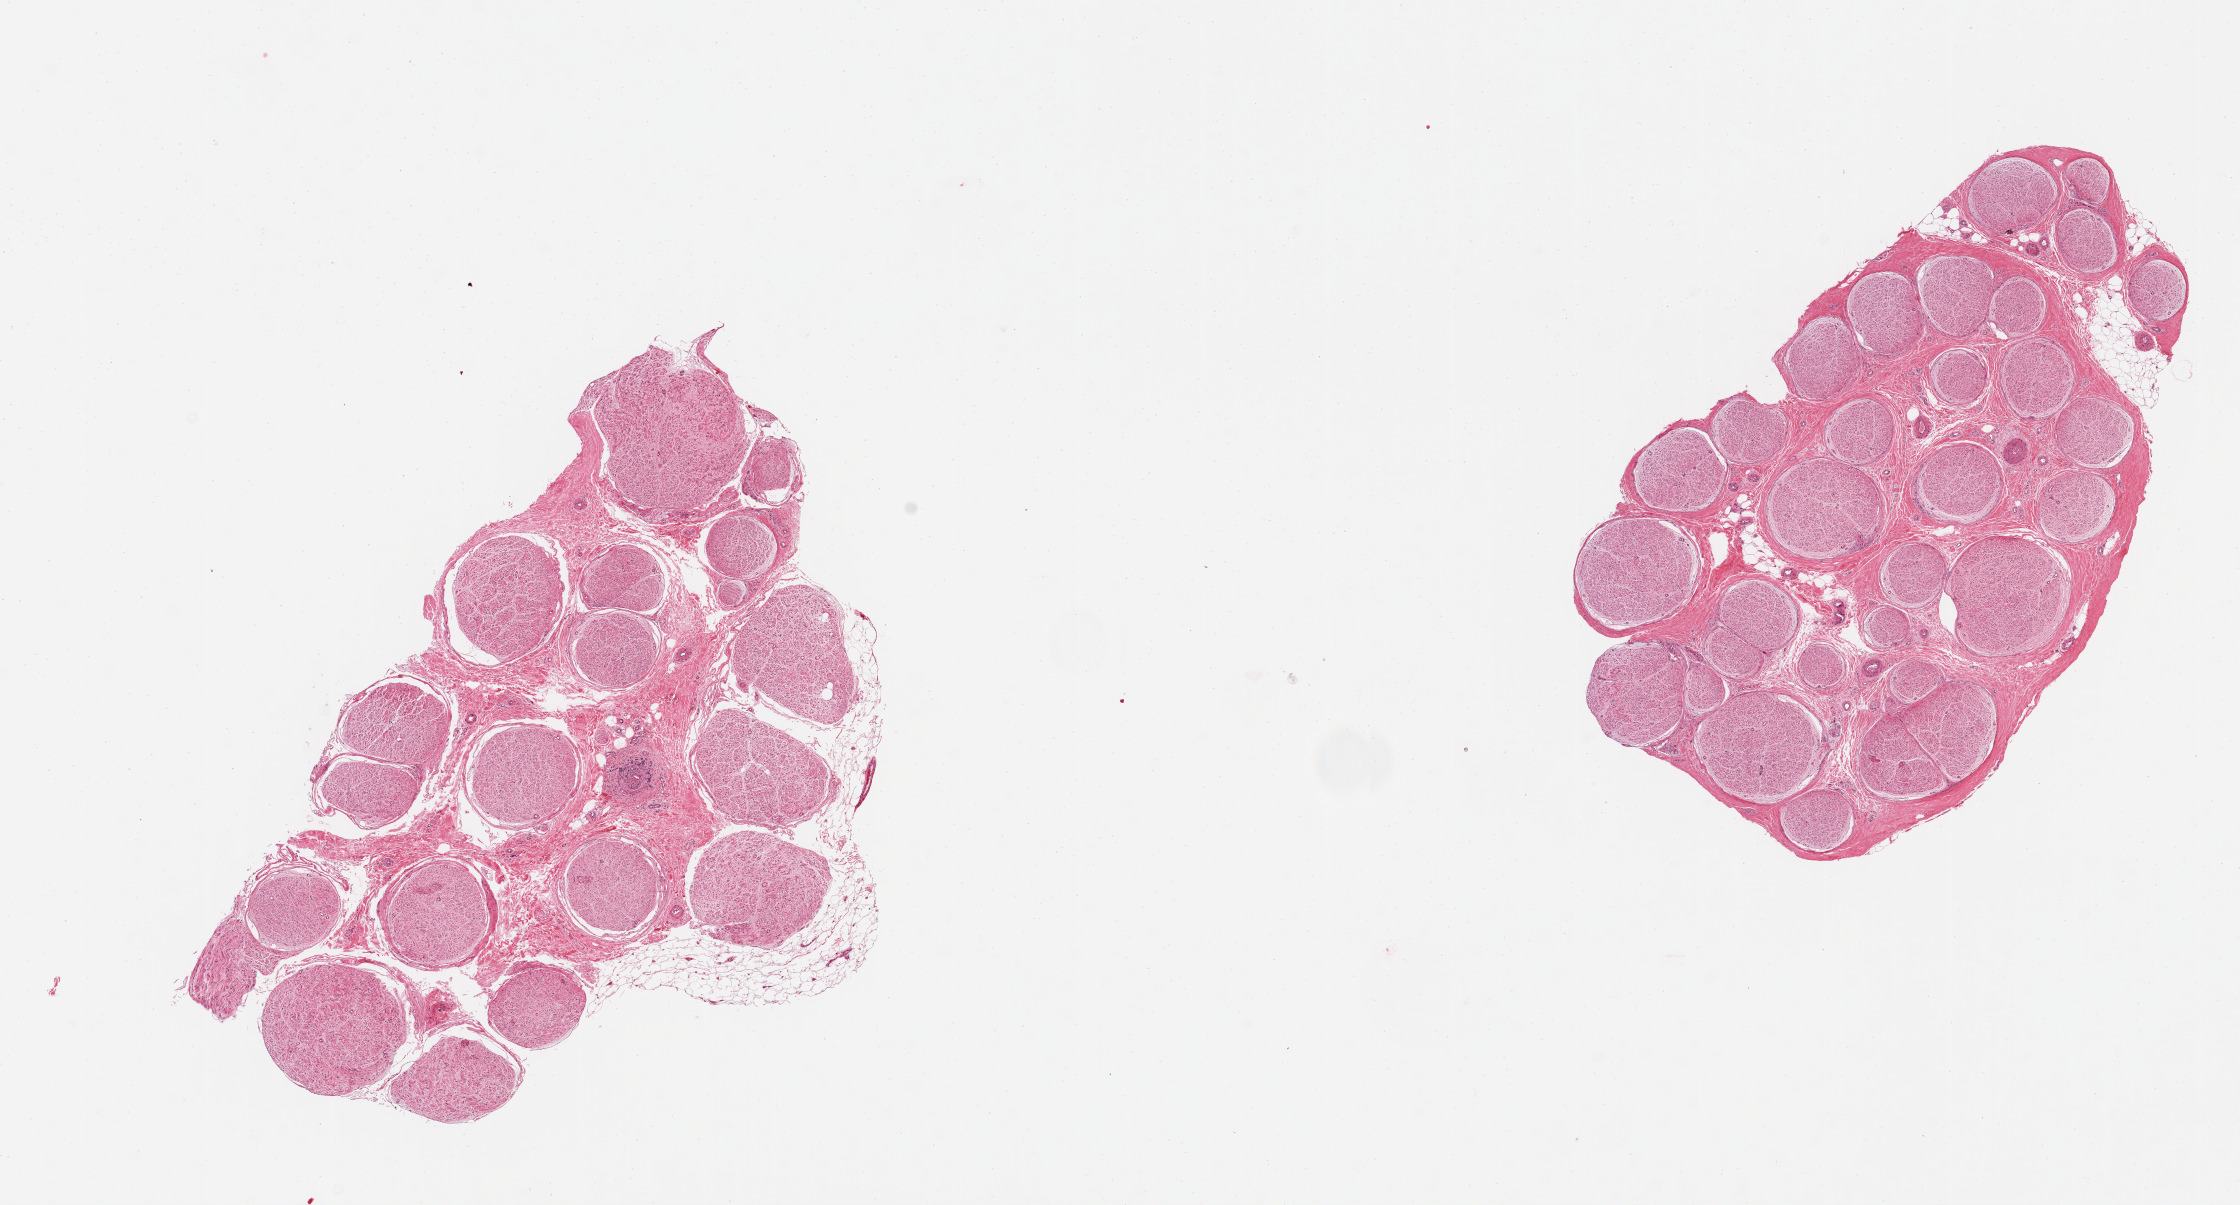
Haematoxylin and eosin whole-slide image, brightfield — whole scanned area (about 17.7 x 9.5 mm, from a 20x scan) shown as a low-resolution overview, PAXgene-fixed, paraffin-embedded tissue, sampled site (target tissue): tibial nerve, tissue donor sample. Donor: male.
Pathologist's review note for this sample: 6 pieces; 5% internal fat.